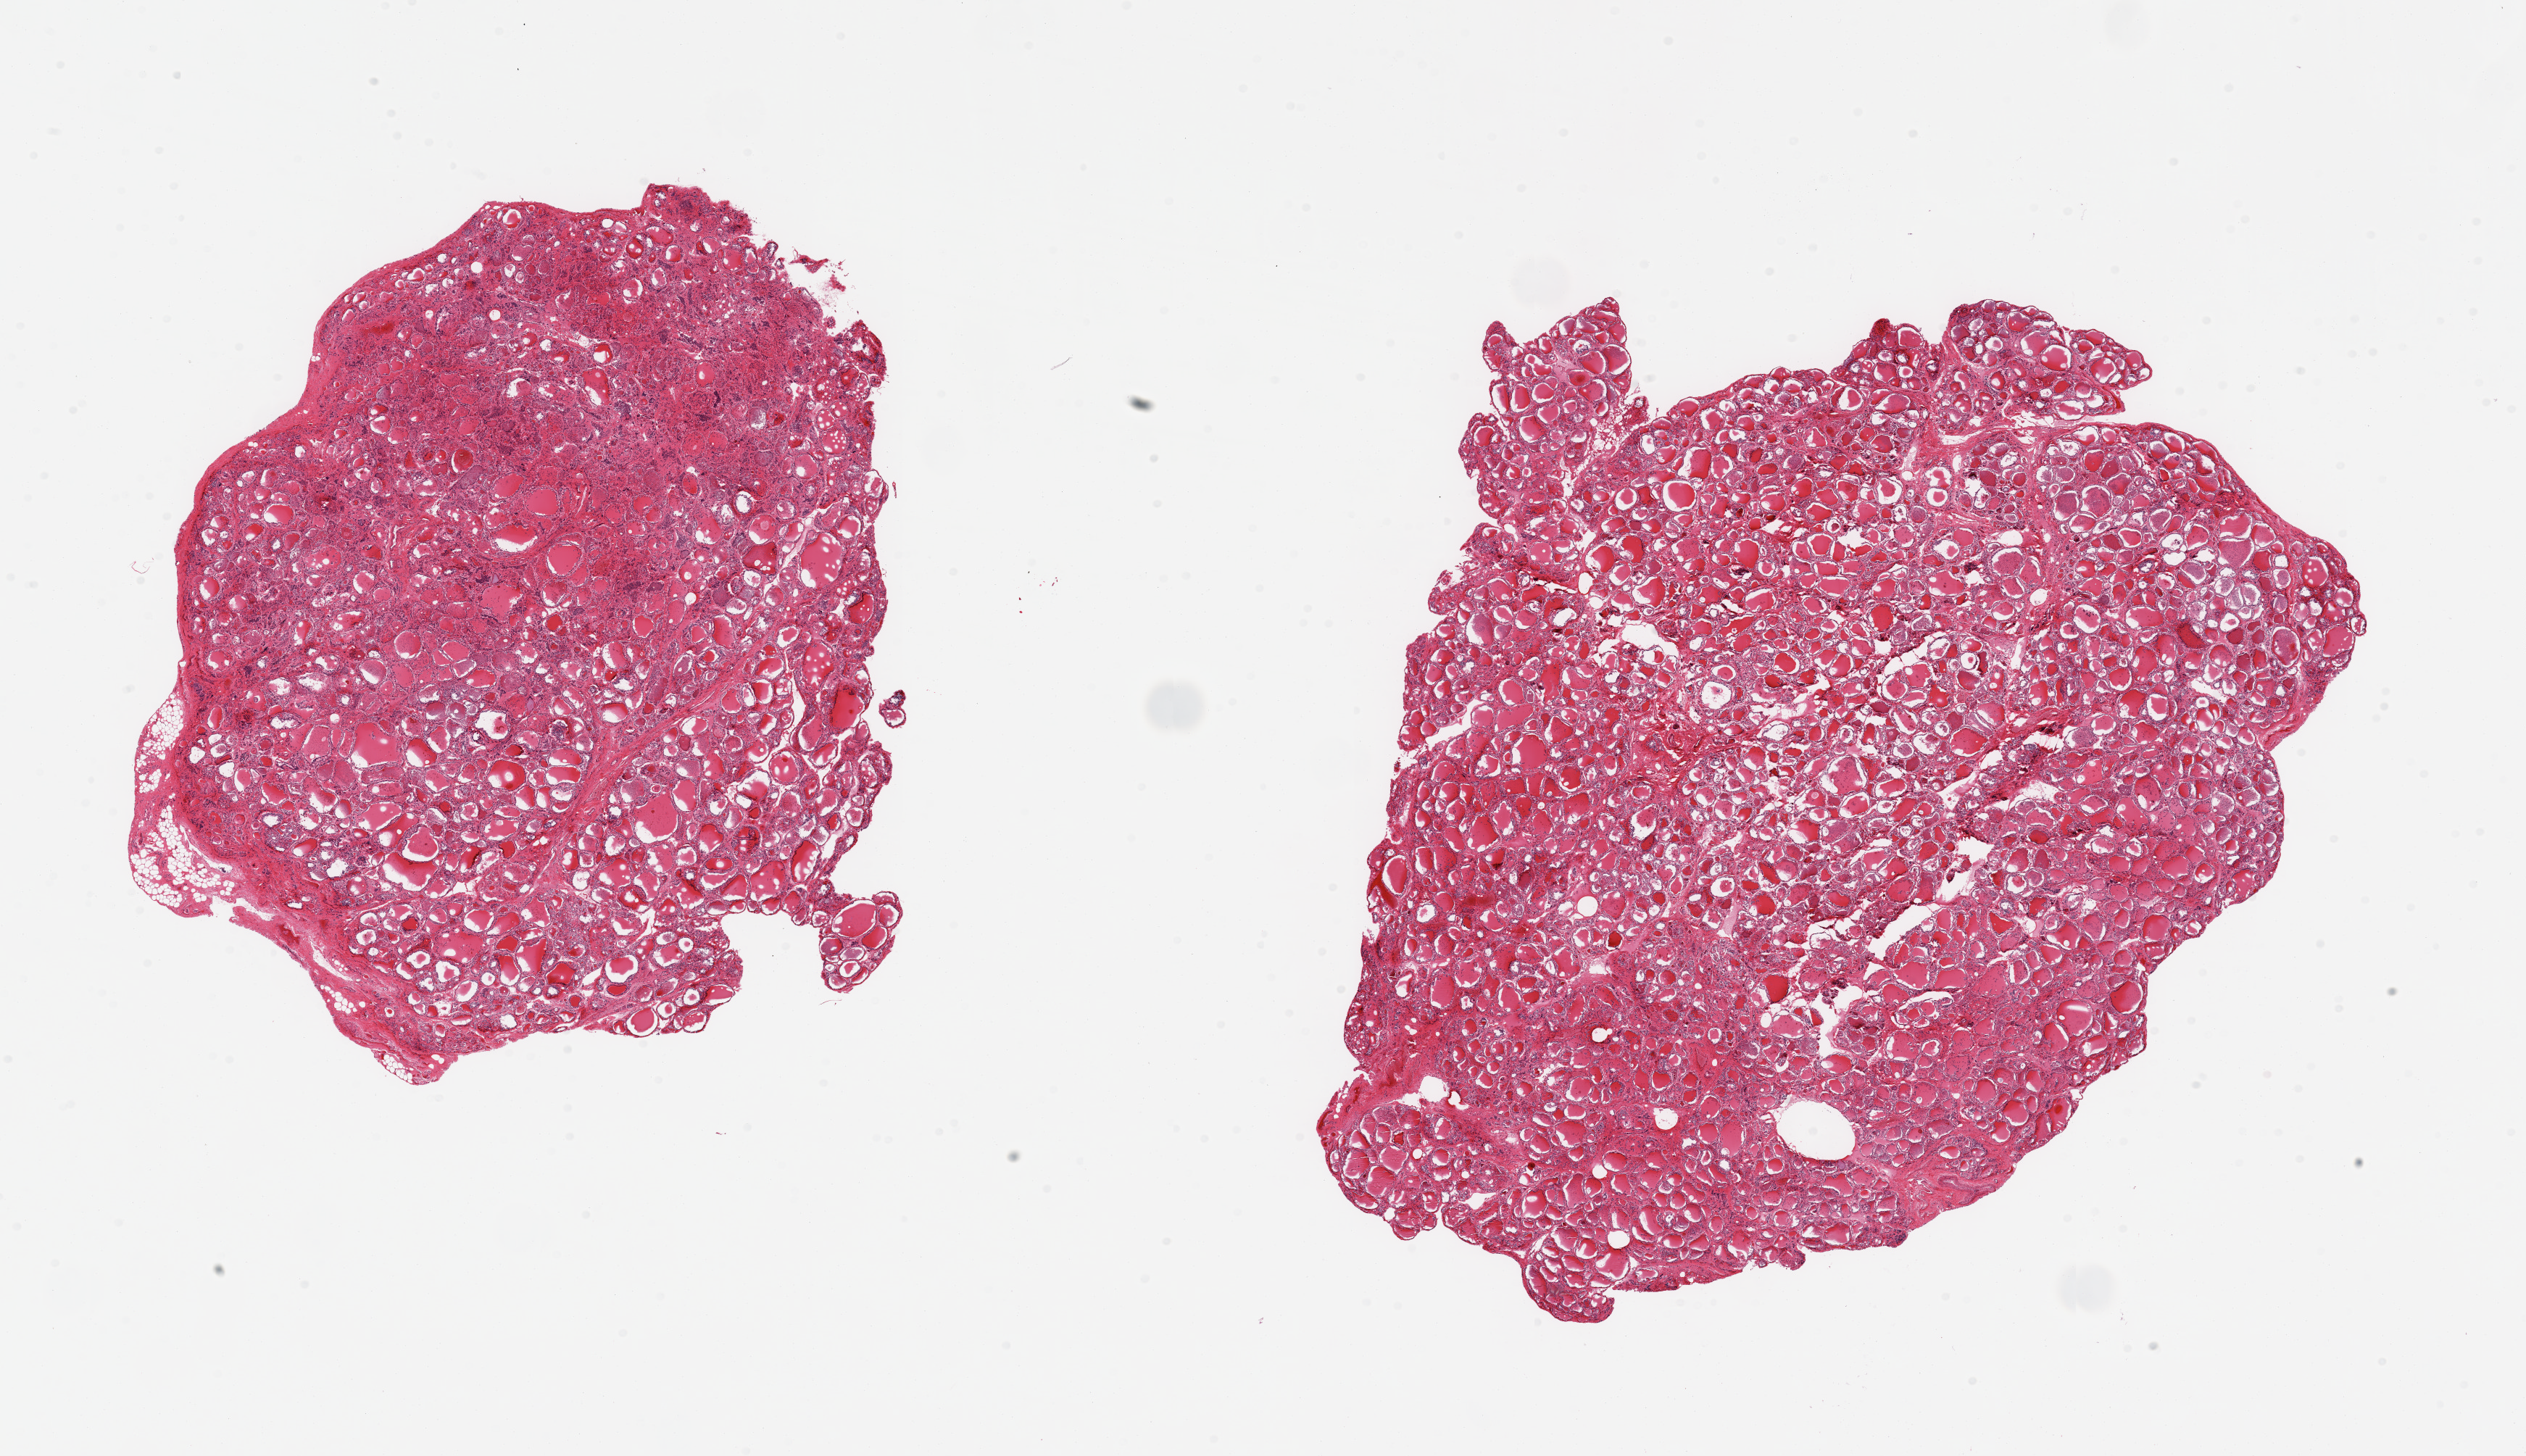
H&E whole-slide image, brightfield, whole scanned area (about 27.6 x 15.9 mm, from a 20x scan) shown as a low-resolution overview, PAXgene-fixed paraffin-embedded (PFPE) section, target tissue: thyroid, tissue donor sample. Male donor.
- review note (as recorded): 2 pieces; poorly preserved follicular lining cells